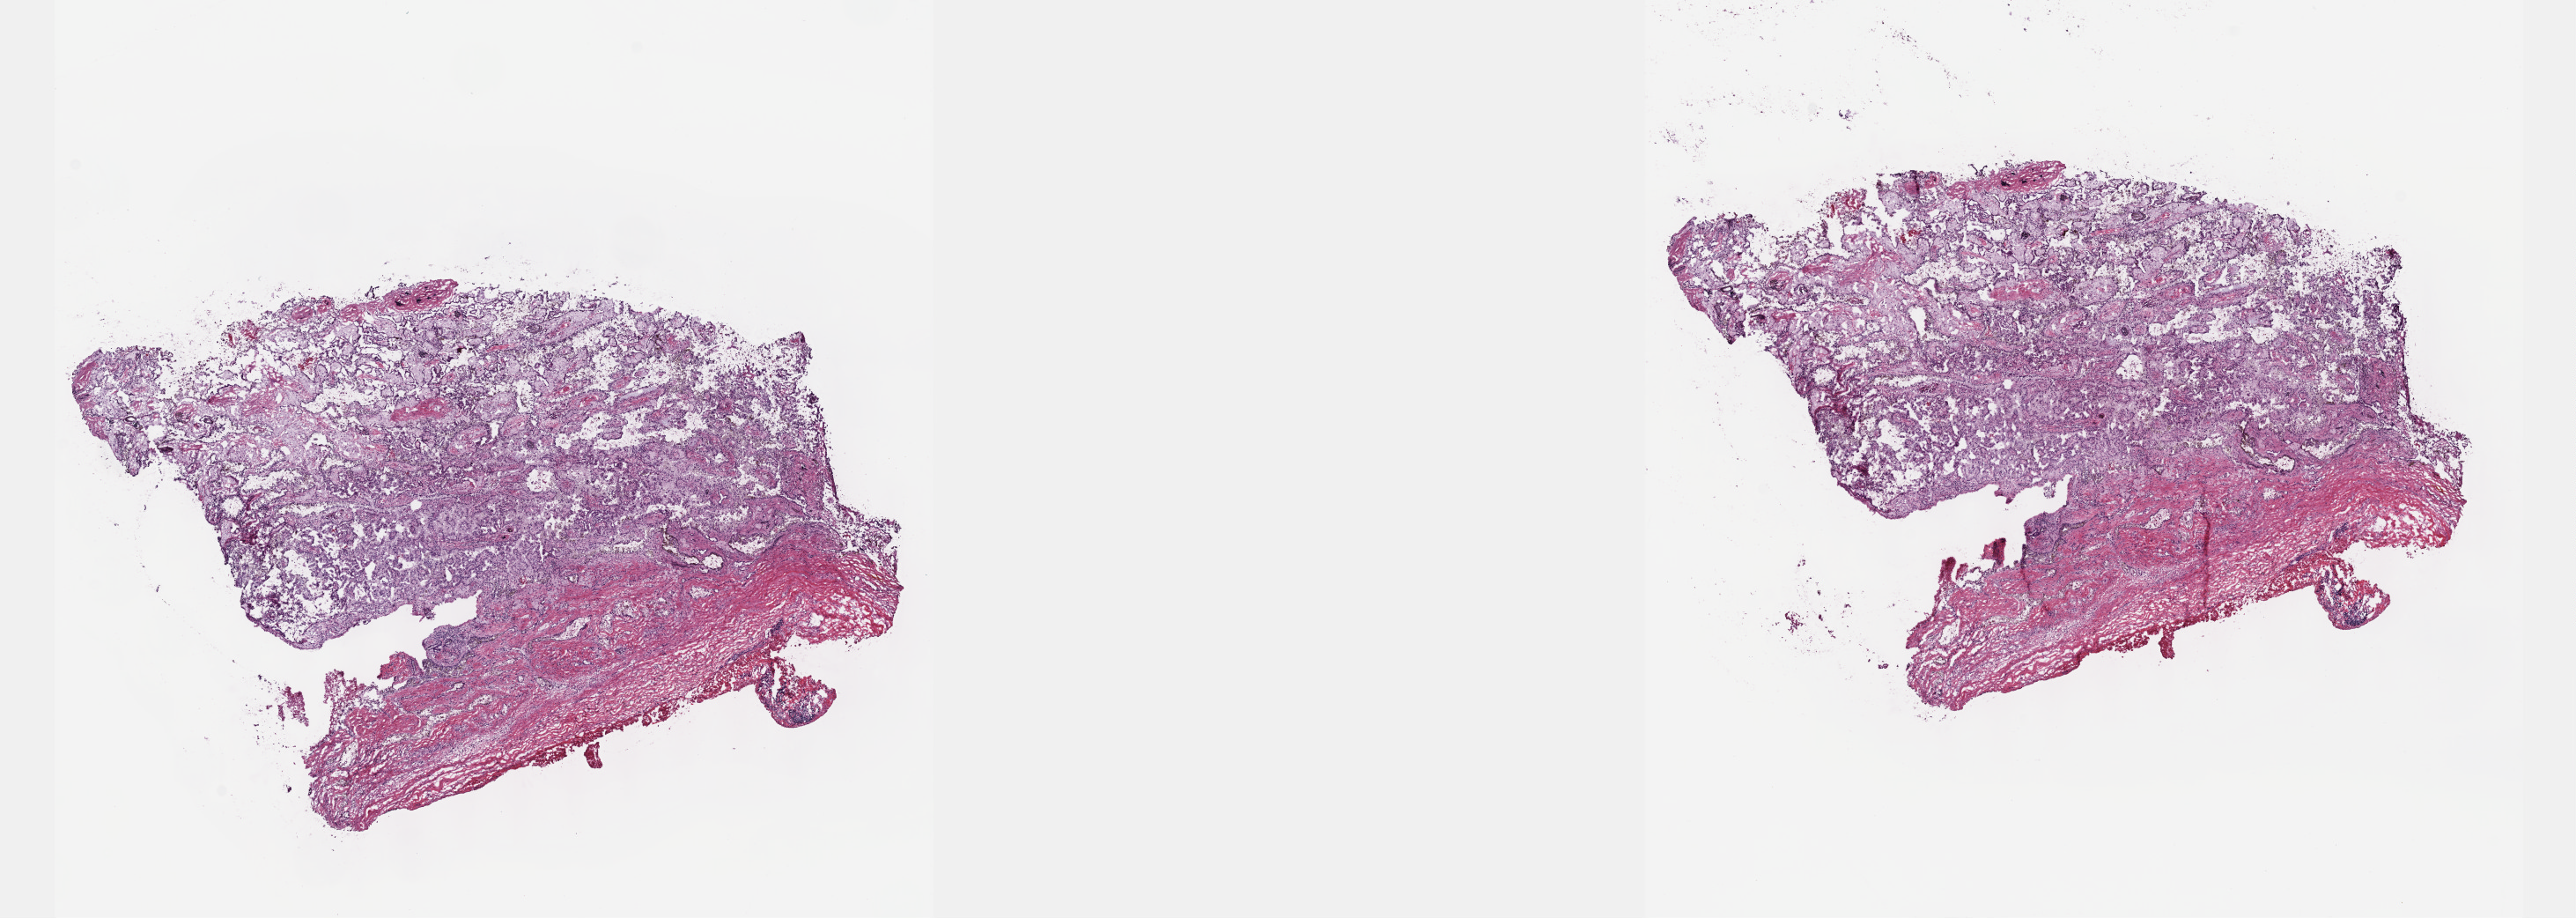
H&E whole-slide image — low-resolution overview of the scanned area, about 23.6 x 8.4 mm (acquisition: 40x scan); frozen section from the top of the tissue portion; primary tumour sample from the kidney. Male, age 63 years at initial diagnosis. Pathologist review of this section (percent, as recorded): tumour cells 40%, tumour nuclei 80%, normal cells 0%, stromal cells 50%, necrosis 10%. Inflammatory infiltration, as recorded: lymphocyte infiltration 4%, monocyte infiltration 10%, neutrophil infiltration 3%.
Histologic diagnosis: Papillary adenocarcinoma, NOS. AJCC pathologic stage: I (5th edition).